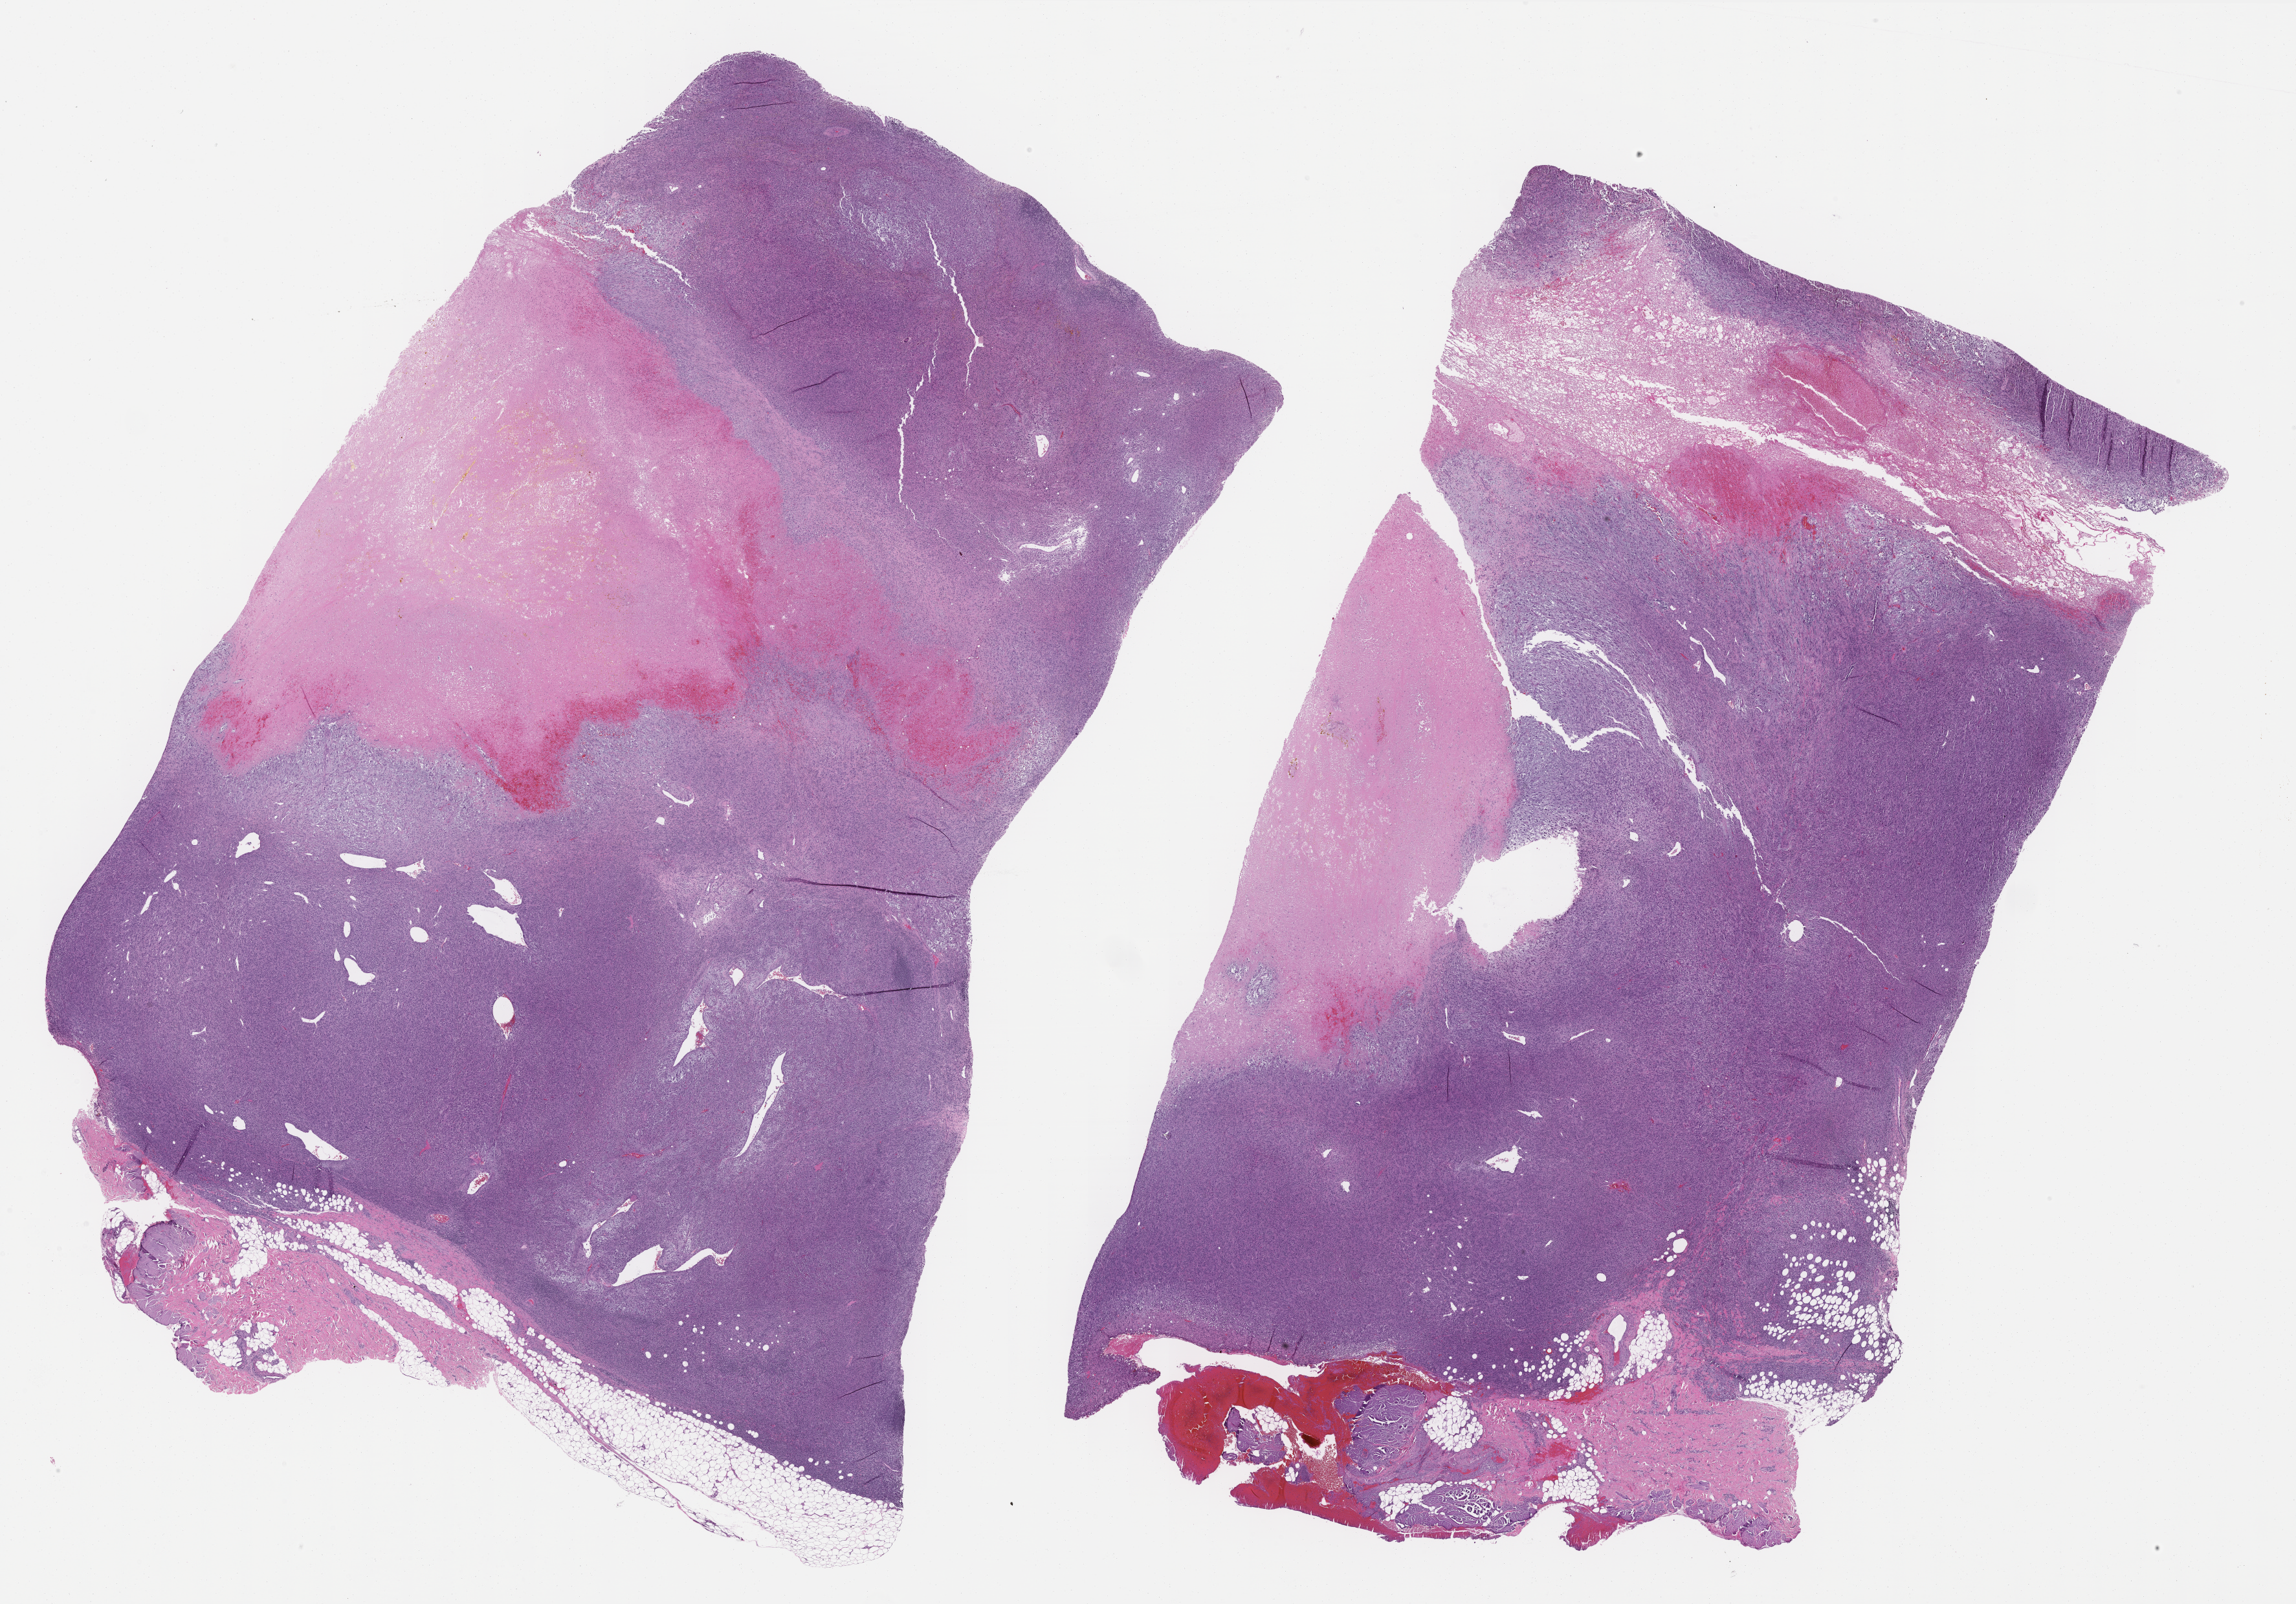
Whole-slide histology image, H&E, shown as a low-resolution overview of the whole scanned area (about 28.5 x 19.9 mm); formalin-fixed paraffin-embedded (FFPE) diagnostic section; primary tumour sample from the connective, subcutaneous and other soft tissues. Male, age 63 years at initial diagnosis.
- pathologic diagnosis: Malignant fibrous histiocytoma (connective, subcutaneous and other soft tissues of lower limb and hip)